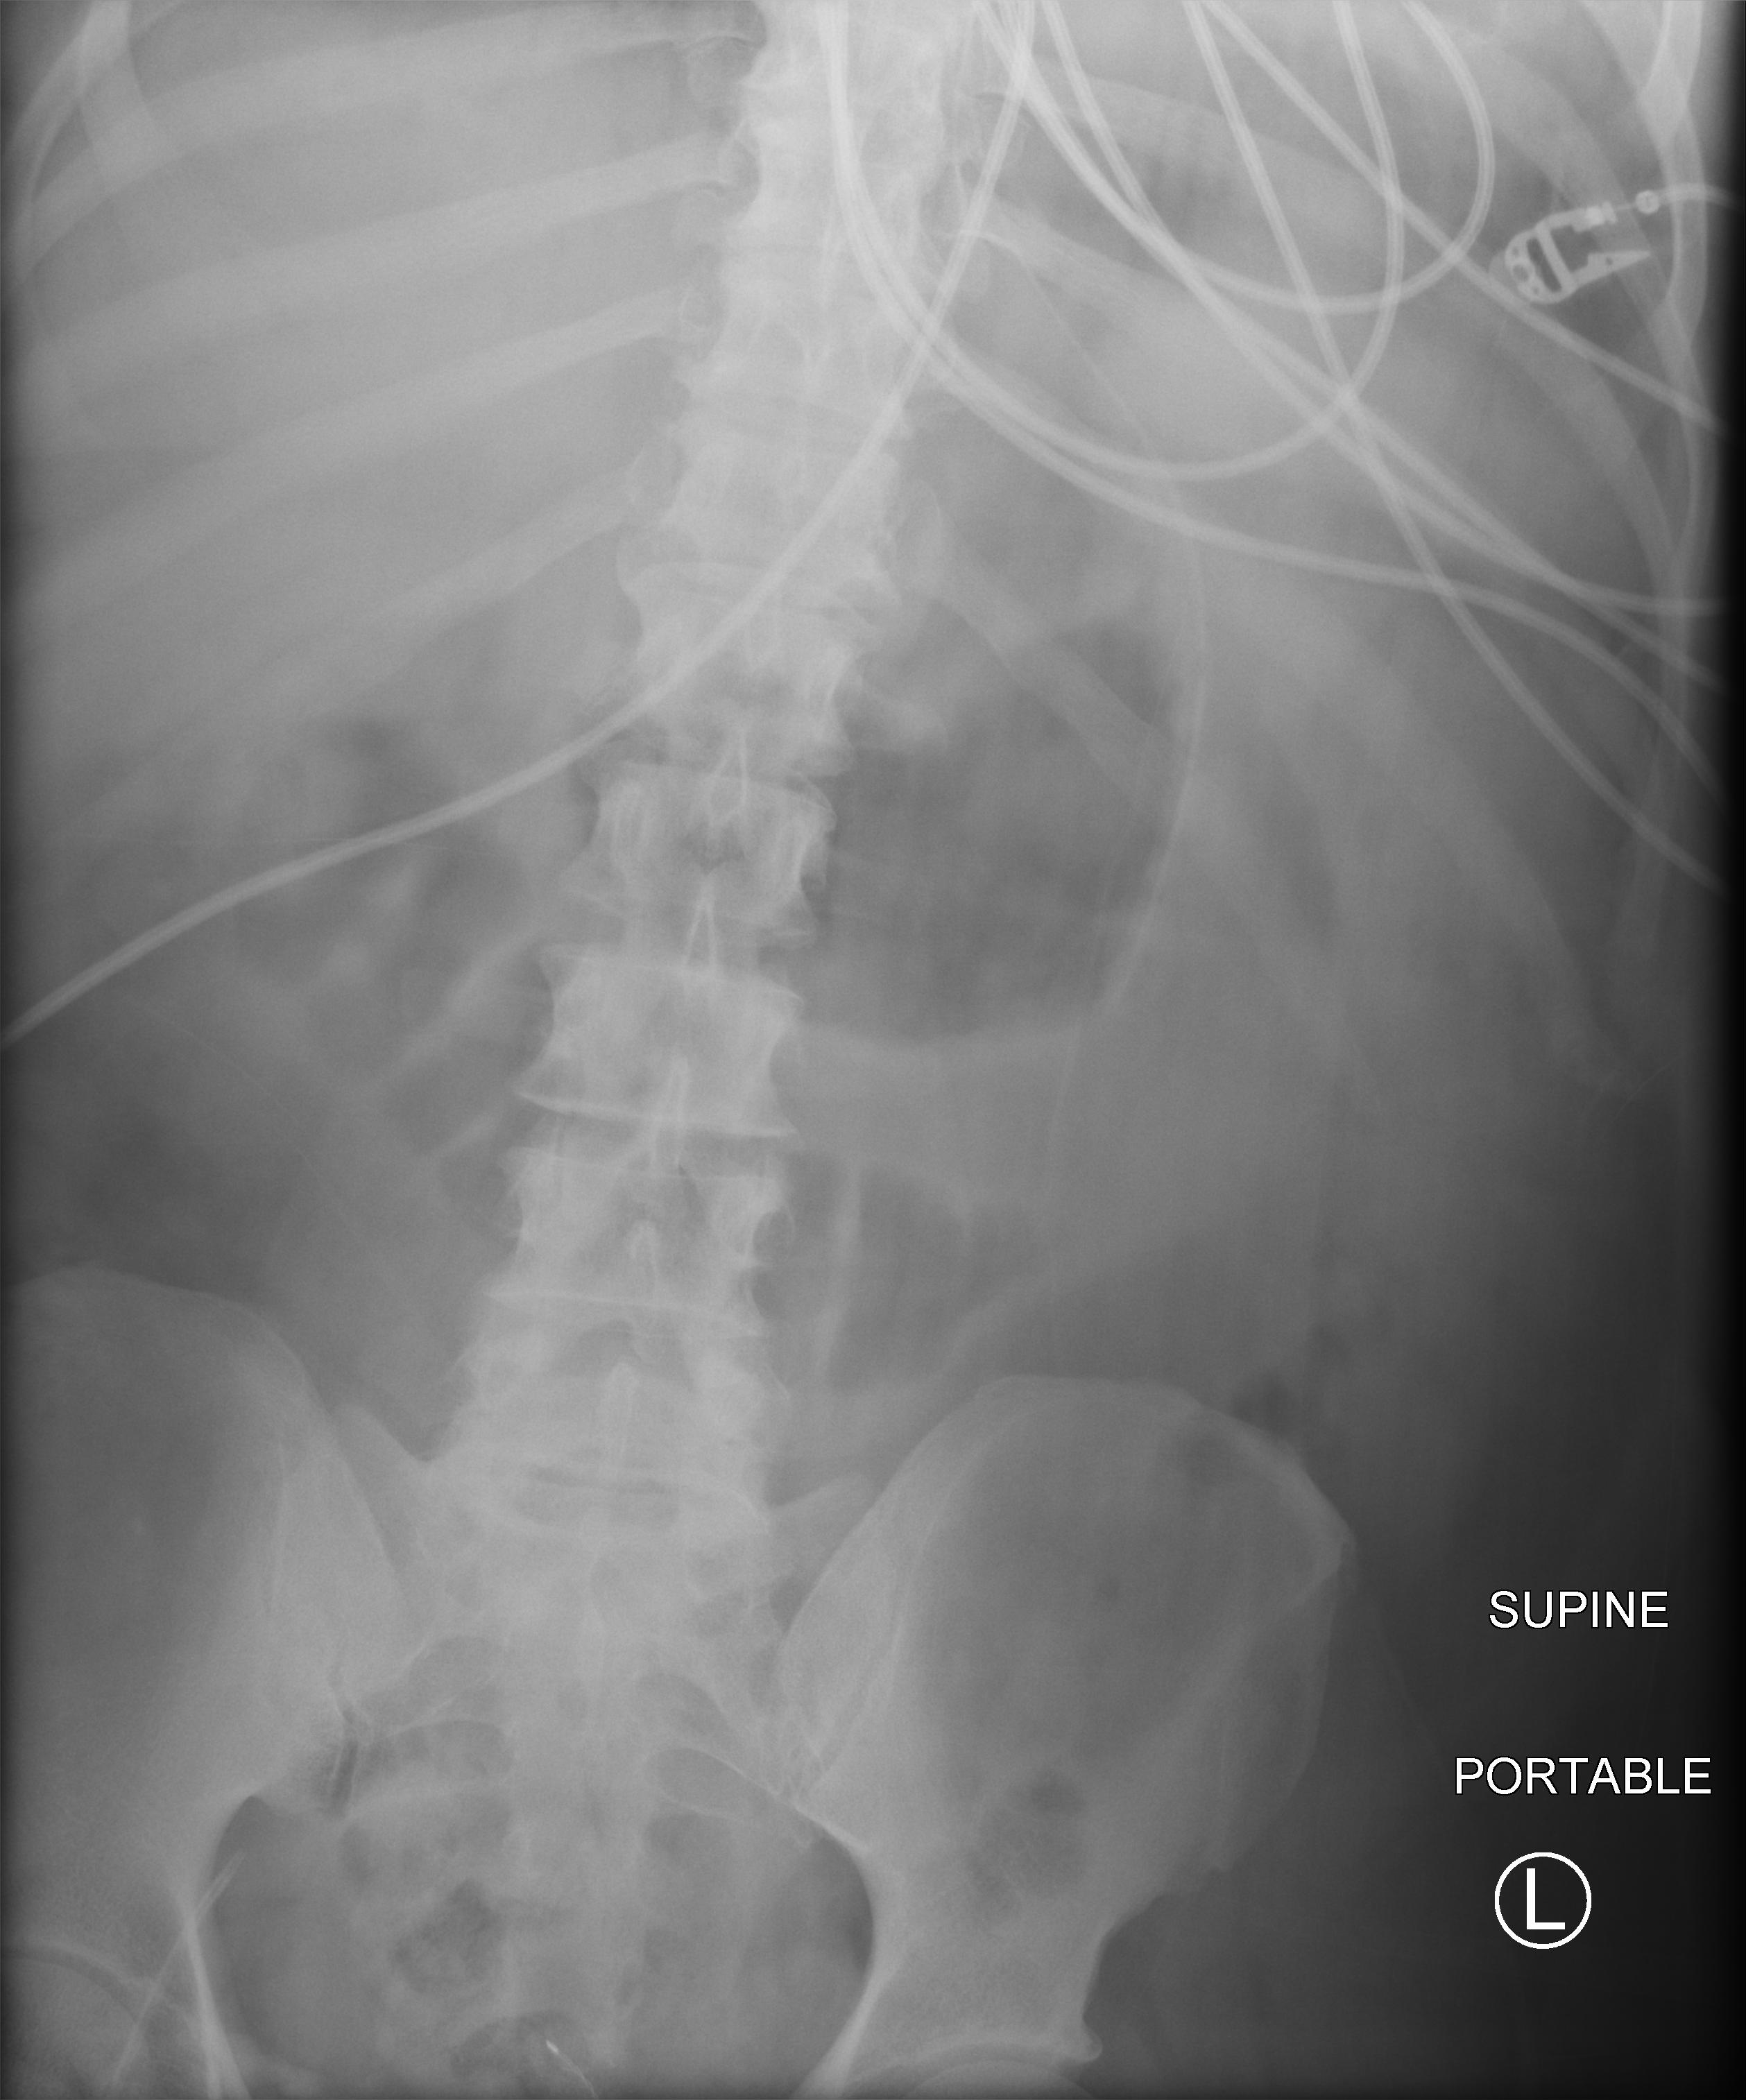
Abdomen X-ray (portable), anteroposterior (AP) projection. Patient hospitalised with COVID-19; male, aged 60–74 years.
From the hospital-stay record, not from the radiograph (when in the stay this image was taken is not recorded): admitted to intensive care during this hospital stay: yes.